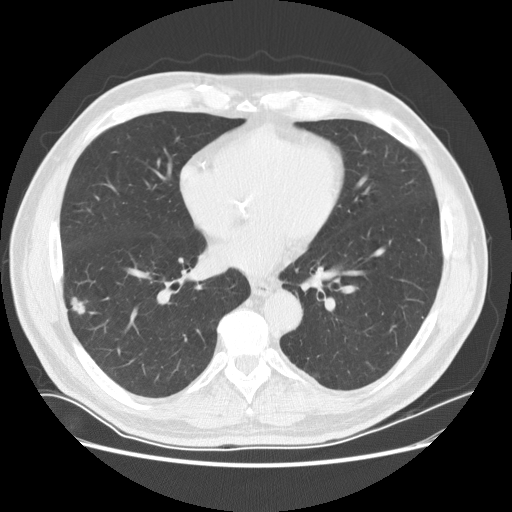
Low-dose screening chest CT, one axial slice; position 76 of 169 along the scan axis; 120 kVp; lung window (W 1500 / L -600 HU); 512 × 512 image matrix.
Outlined on this slice (manually delineated by an expert):
- lesion 1 (tumor, lower lobe of right lung): bounding box <71,297,85,315> (left, top, right, bottom; pixels)